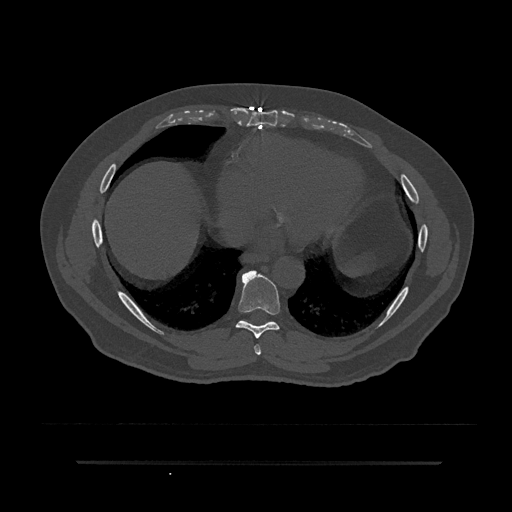
CT including the spine, one axial slice; slice 421 of 797 in the series (ordered by position); reconstruction kernel Br40s/3; bone window (W 1800 / L 400 HU); 0.5 mm slice thickness; 512 × 512 image matrix, field of view 464 × 464 mm. Patient: male, 59 years. Case-level facts recorded for this patient, not image findings: primary cancer: bile ducts; vertebrae with lytic lesions (as recorded): T10.
Structures marked on this image (semi-automatically segmented with operator editing):
- T7 vertebra: bounding box <254,344,261,355> (left, top, right, bottom; pixels)
- T8 vertebra: <236,270,280,339>